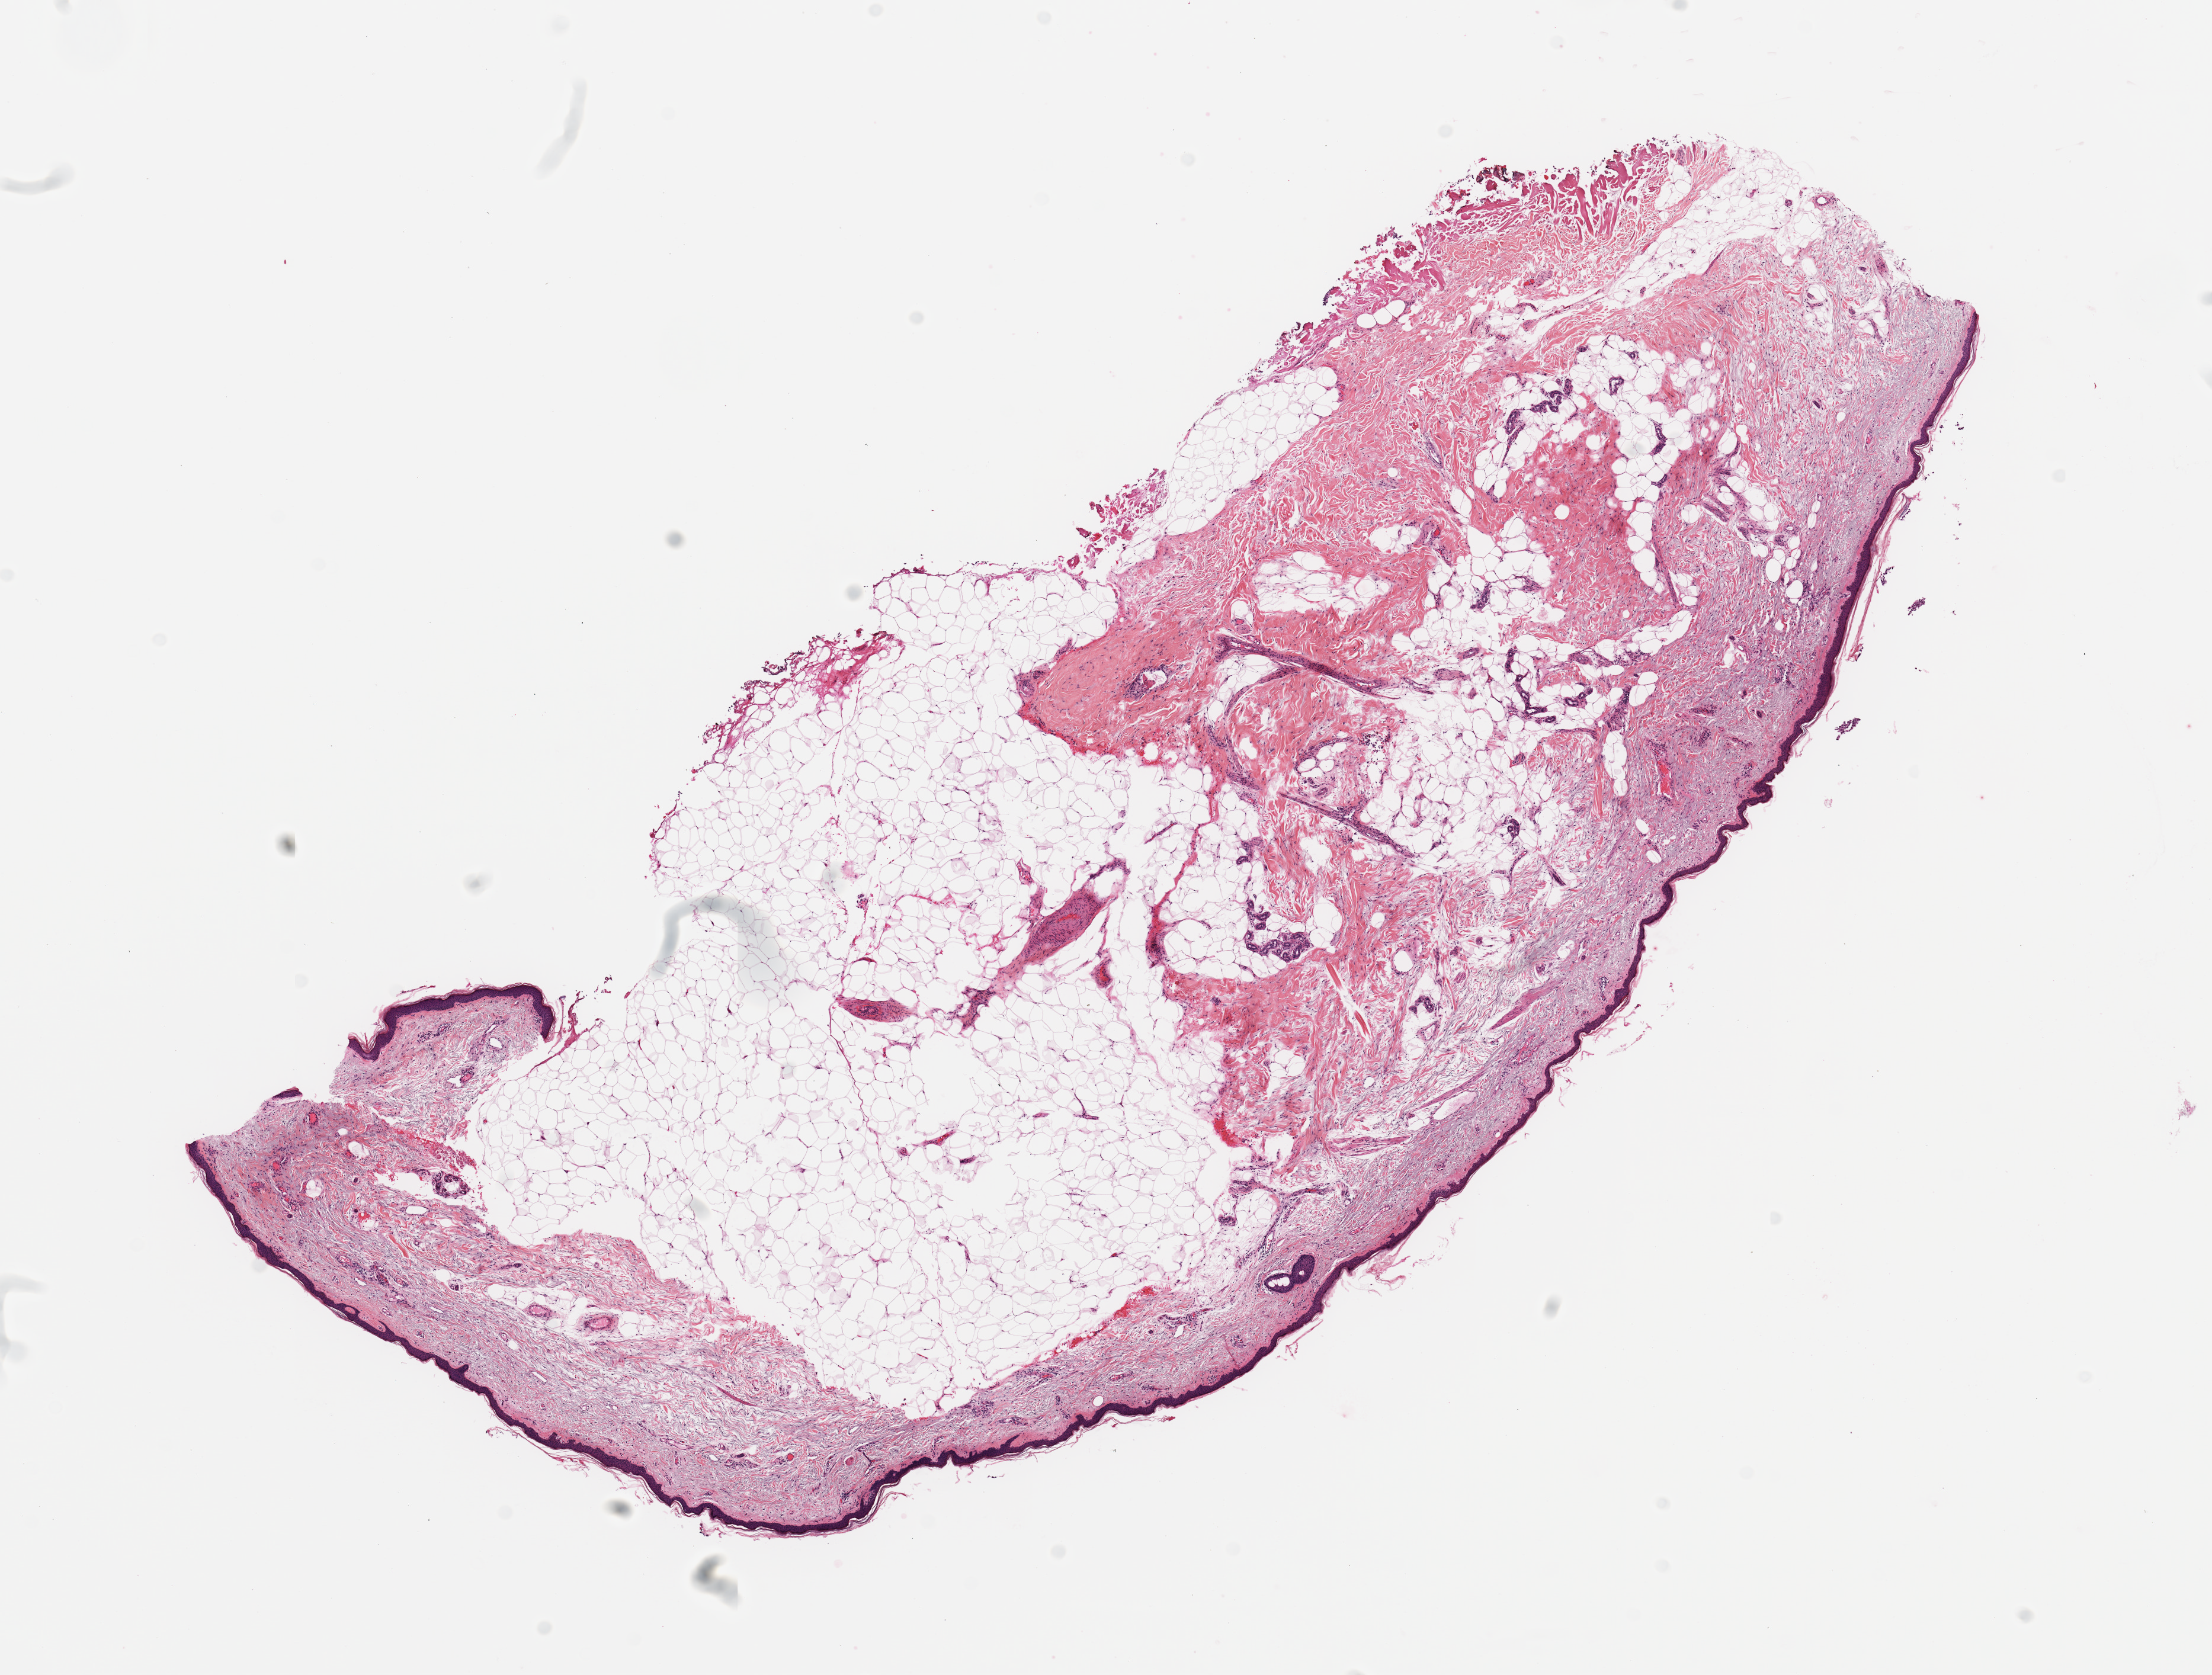
Digitized H&E-stained tissue section (whole slide), shown as a low-resolution overview of the whole scanned area (about 14.8 x 11.2 mm), normal (non-tumour) tissue sample, sampled site: skin. 84-year-old female patient.
- this section: normal (non-tumour) tissue from the same patient
- patient diagnosis: Malignant melanoma, NOS